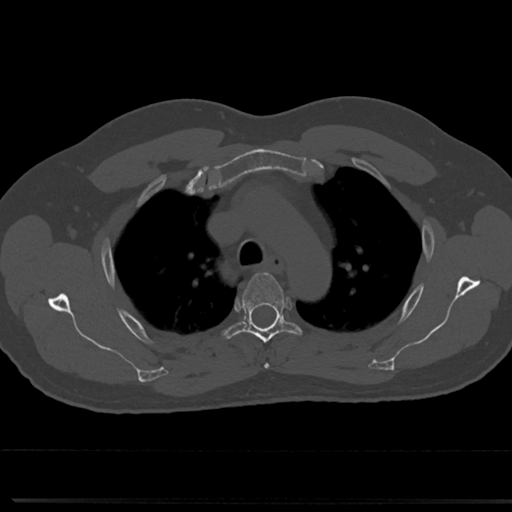
CT including the spine, one axial slice. Position 552 of 817 along the scan axis. Reconstruction kernel Br40s/3. 120 kVp. Bone window (W 1800 / L 400 HU). 0.5 mm slice thickness. 512 × 512 image matrix, field of view 355 × 355 mm. Patient: male, 61 years. From the clinical record (not read from this slice): primary cancer: prostate.
Structures marked on this image (semi-automatically segmented with operator editing):
- T3 vertebra: box from (x=264, y=363) to (x=269, y=368) px
- T4 vertebra: (x=220, y=273)–(x=301, y=344)